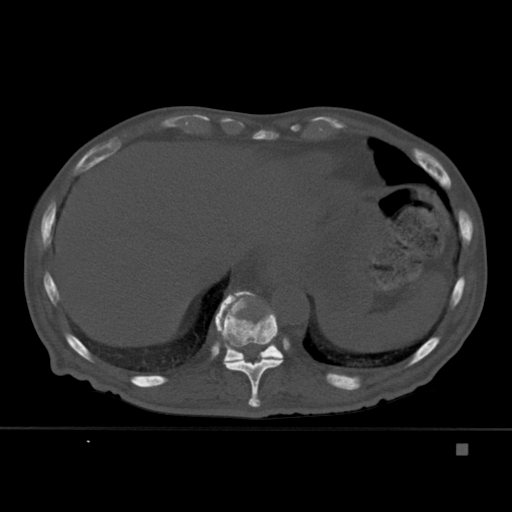
CT including the spine, one axial slice. Slice 227 of 451 in the series (ordered by position). Bone window (W 1800 / L 400 HU). 1.5 mm slice thickness. 512 × 512 image matrix, field of view 378 × 378 mm. Patient: male, 75 years. Case-level facts recorded for this patient, not image findings: primary cancer: prostate.
Outlined on this slice (semi-automatic segmentation, software-assisted and operator-edited):
- T10 vertebra: bounding box (x1, y1, x2, y2) in pixels: (215, 290, 283, 408)
- T11 vertebra: (215, 296, 284, 363)